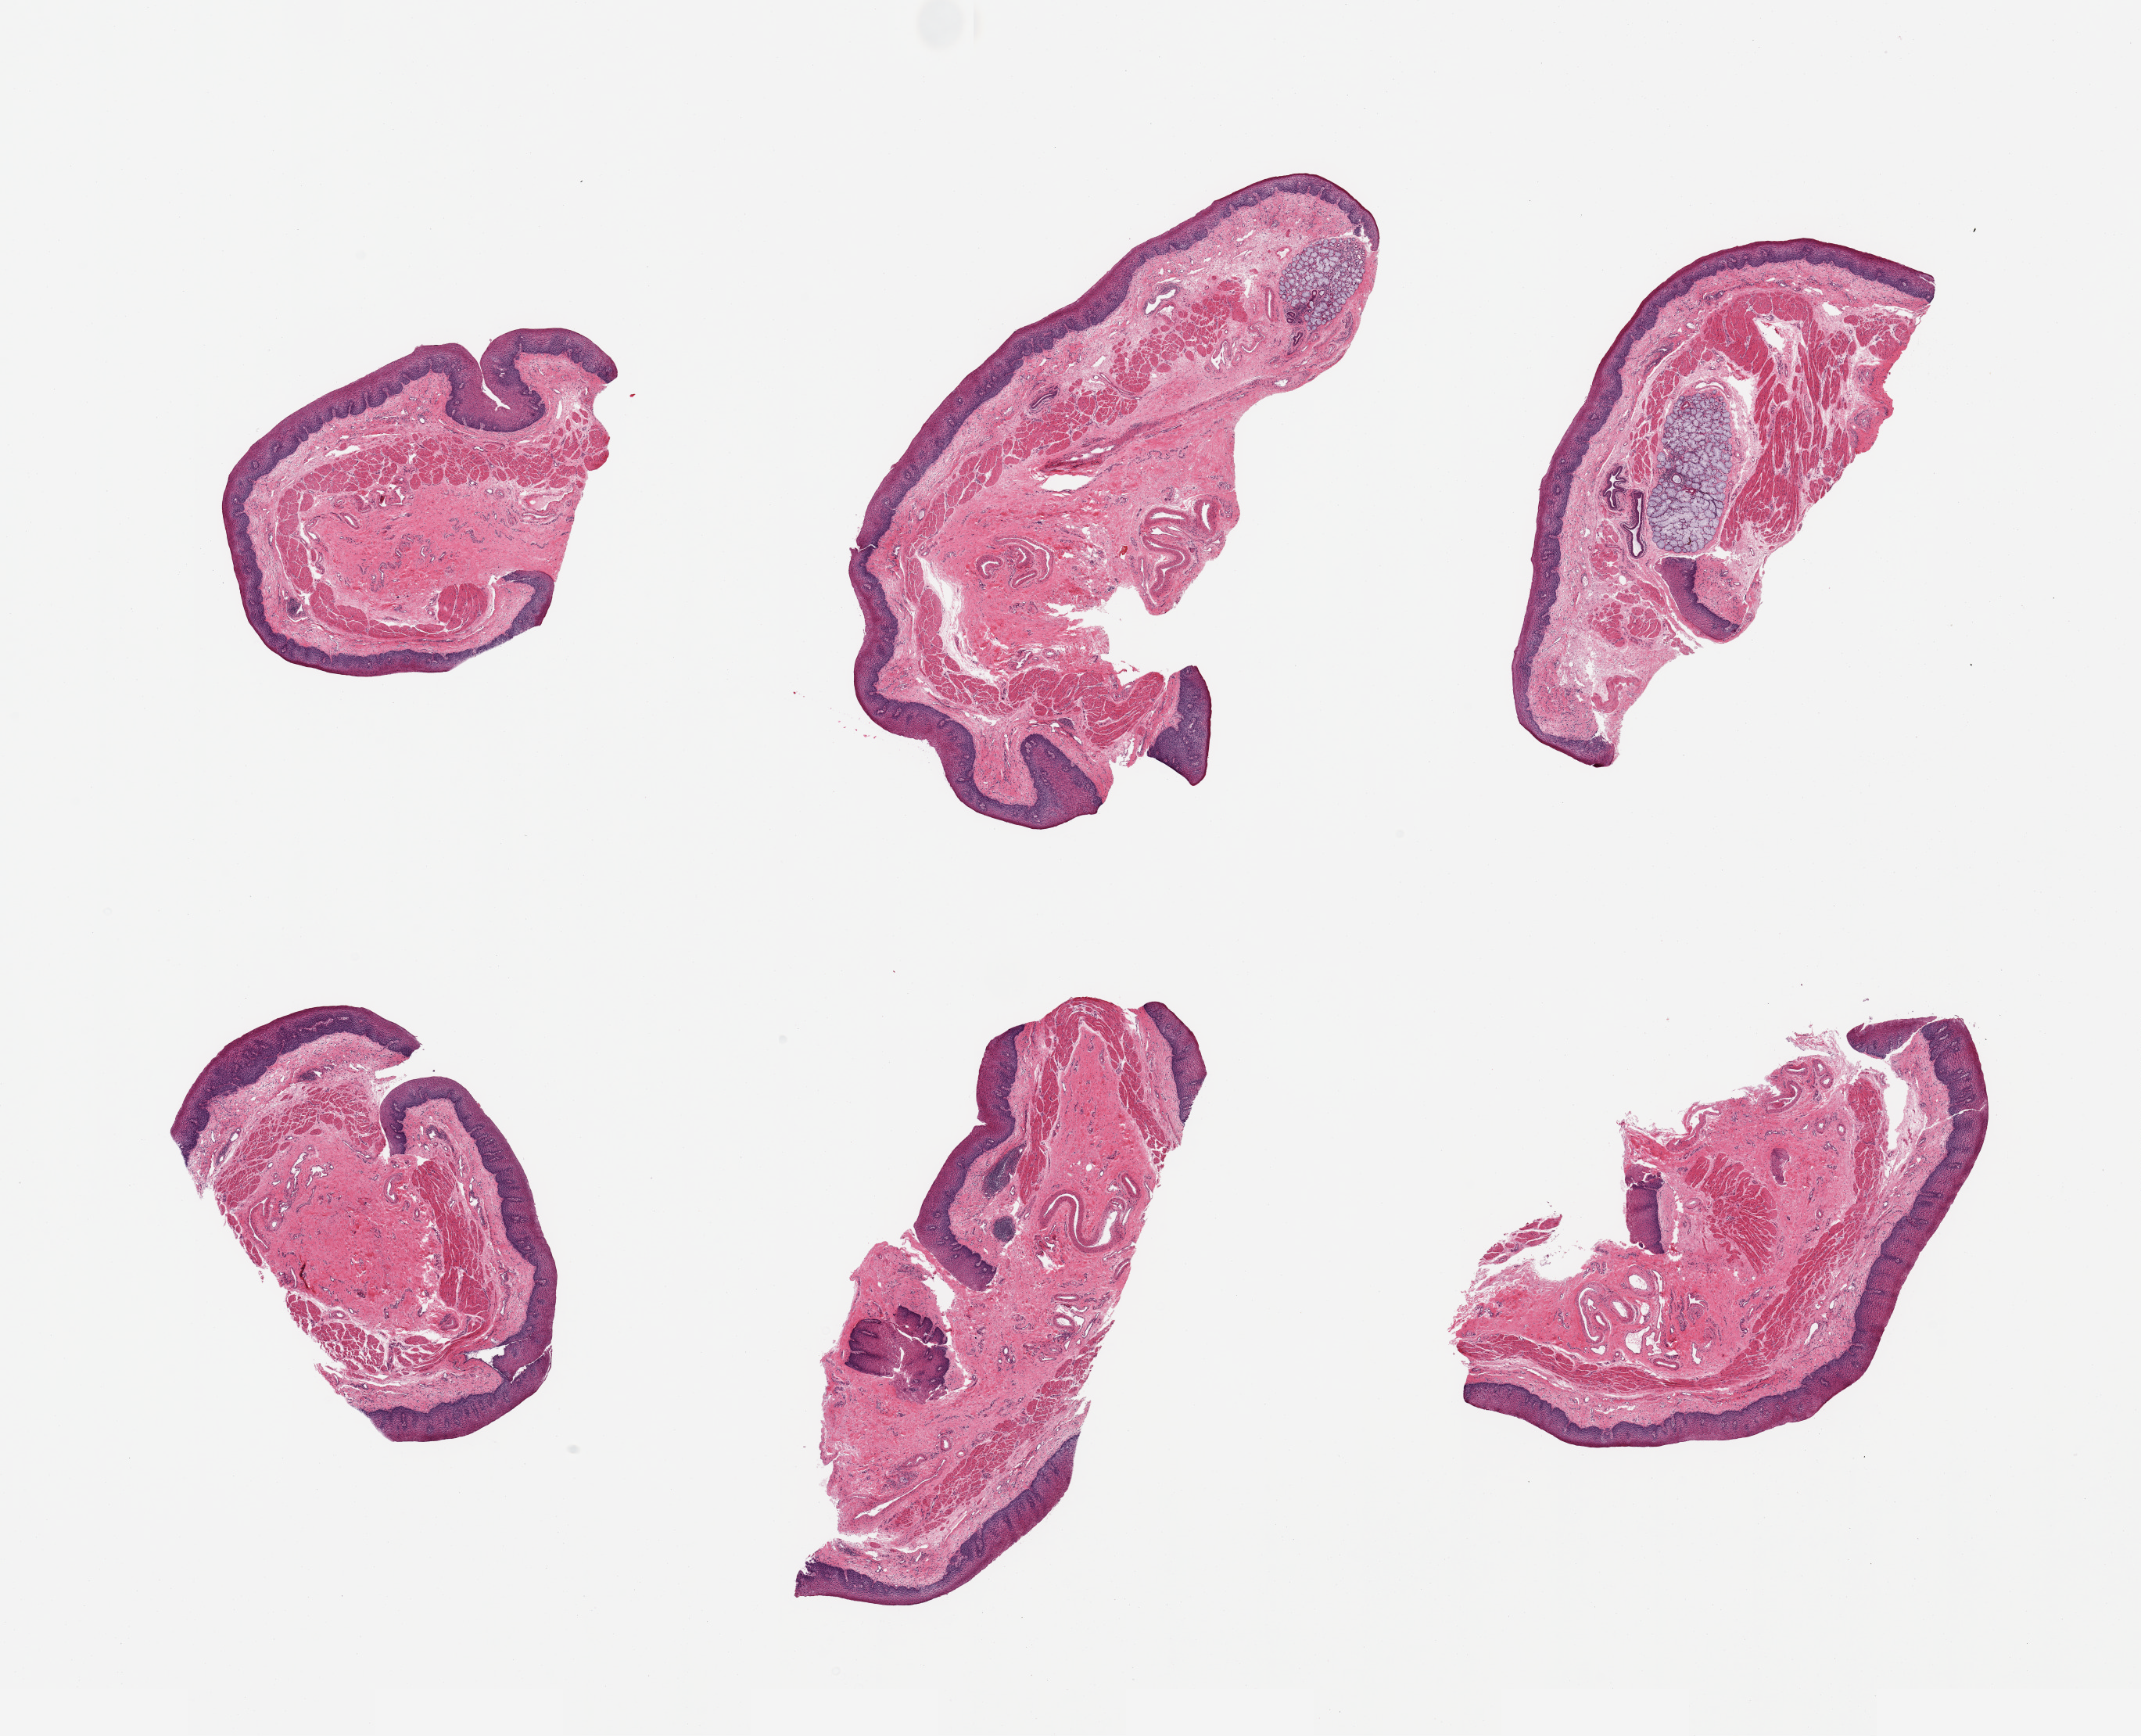
Digitized H&E-stained section, a low-resolution overview of the entire scanned area, about 21.7 x 17.6 mm (slide scanned at 20x); PAXgene-fixed, paraffin-embedded tissue; target tissue: esophageal mucous membrane; tissue donor sample. Male donor.
Review note (as recorded): 6 pieces; squamous mucosa up to 0.3mm, submucosal mucus glands noted.